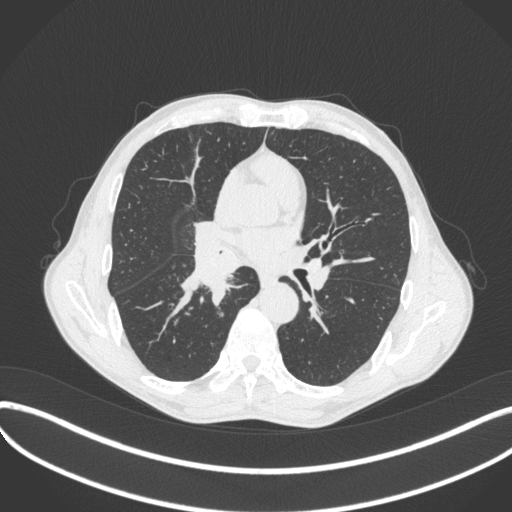
Chest CT, one axial slice. Slice 230 of 481 in the series (ordered by position). 120 kVp. Lung window (W 1500 / L -600 HU). 1 mm slice thickness. 512 × 512 image matrix, field of view 400 × 400 mm. Patient: male, 65 years. Case-level facts recorded for this patient, not image findings: clinical TNM (as recorded): T2a N0 M0; histopathological grade: G2.
Outlined on this slice (bounding box drawn by a radiologist):
- lung tumour (recorded histology: squamous cell carcinoma): bounding box [x1, y1, x2, y2] px = [175, 236, 241, 310]